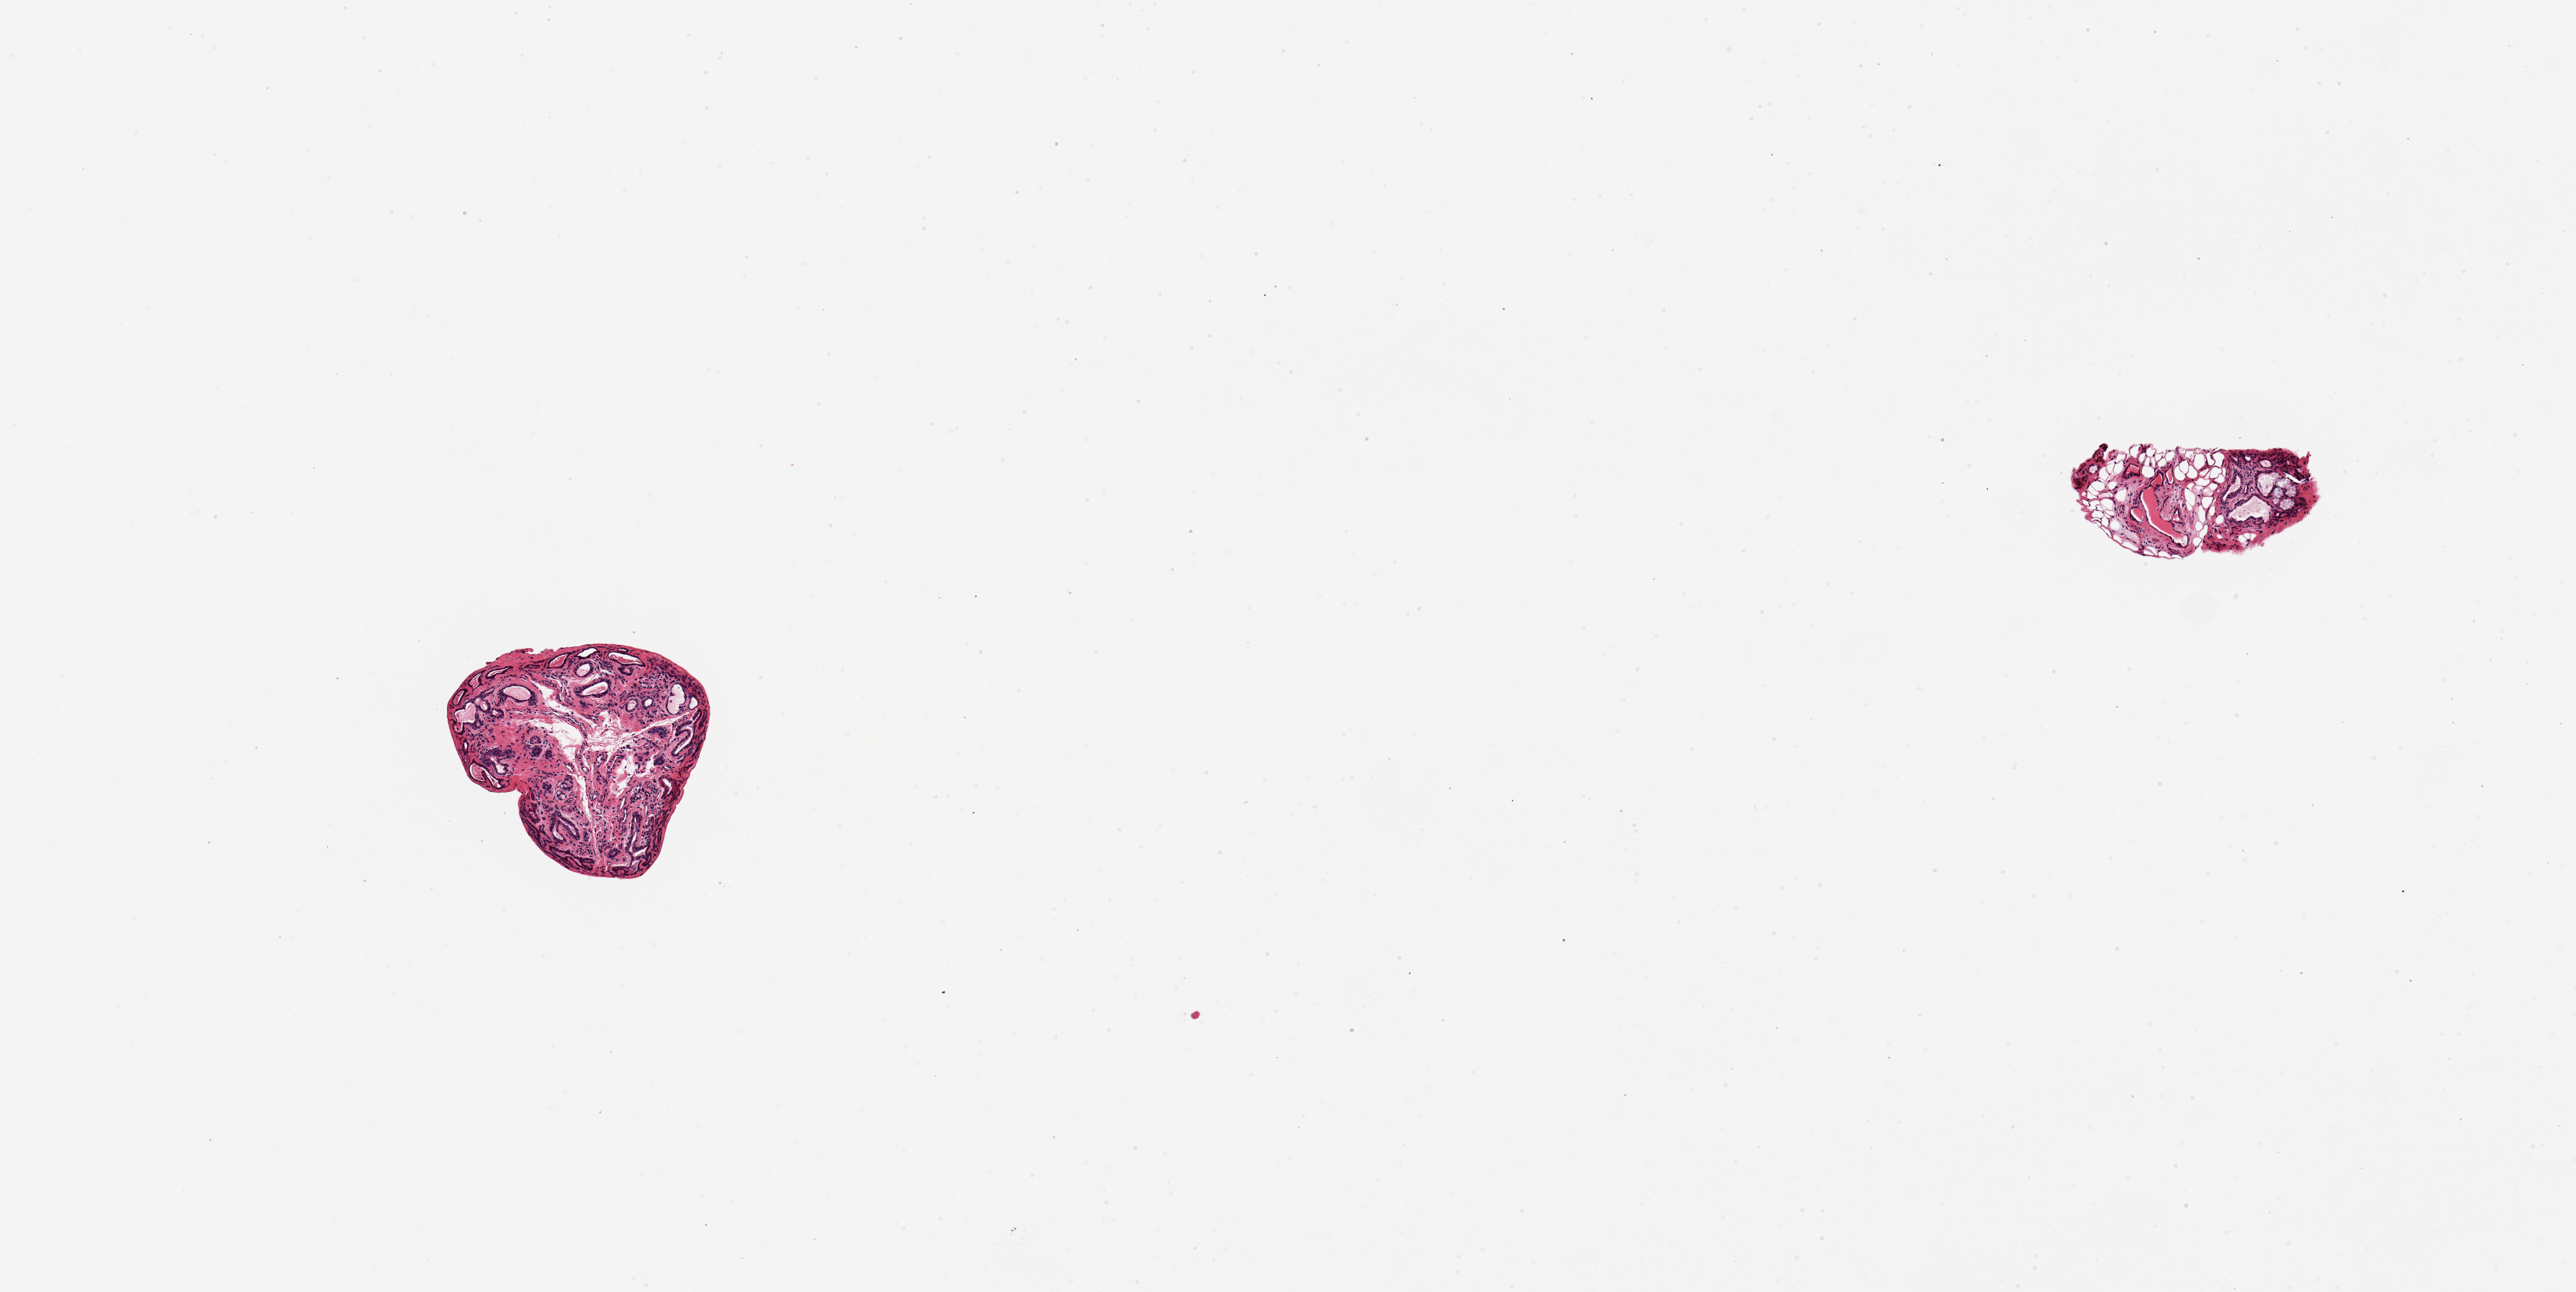
Digitized H&E-stained section, whole scanned area (about 7.9 x 3.9 mm) shown as a low-resolution overview; PAXgene-fixed, paraffin-embedded tissue; sampled site (target tissue): minor salivary gland; donor tissue sample. Female donor.
Reviewer comment on this tissue sample: 2 pieces; one includes some fat.